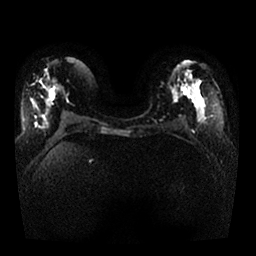
Breast MRI, one axial slice; slice 14 of 25 in the series (ordered by position); diffusion-weighted series; image 2 of 4 stored at this slice position (different b-values; order by instance number); 1.5 T; 4 mm slice thickness; 256 × 256 image matrix, field of view 350 × 350 mm. Female patient.
Outlined on this slice (manually delineated by an expert):
- tumour on diffusion-weighted imaging: bounding box (x1, y1, x2, y2) in pixels: (190, 88, 198, 97)